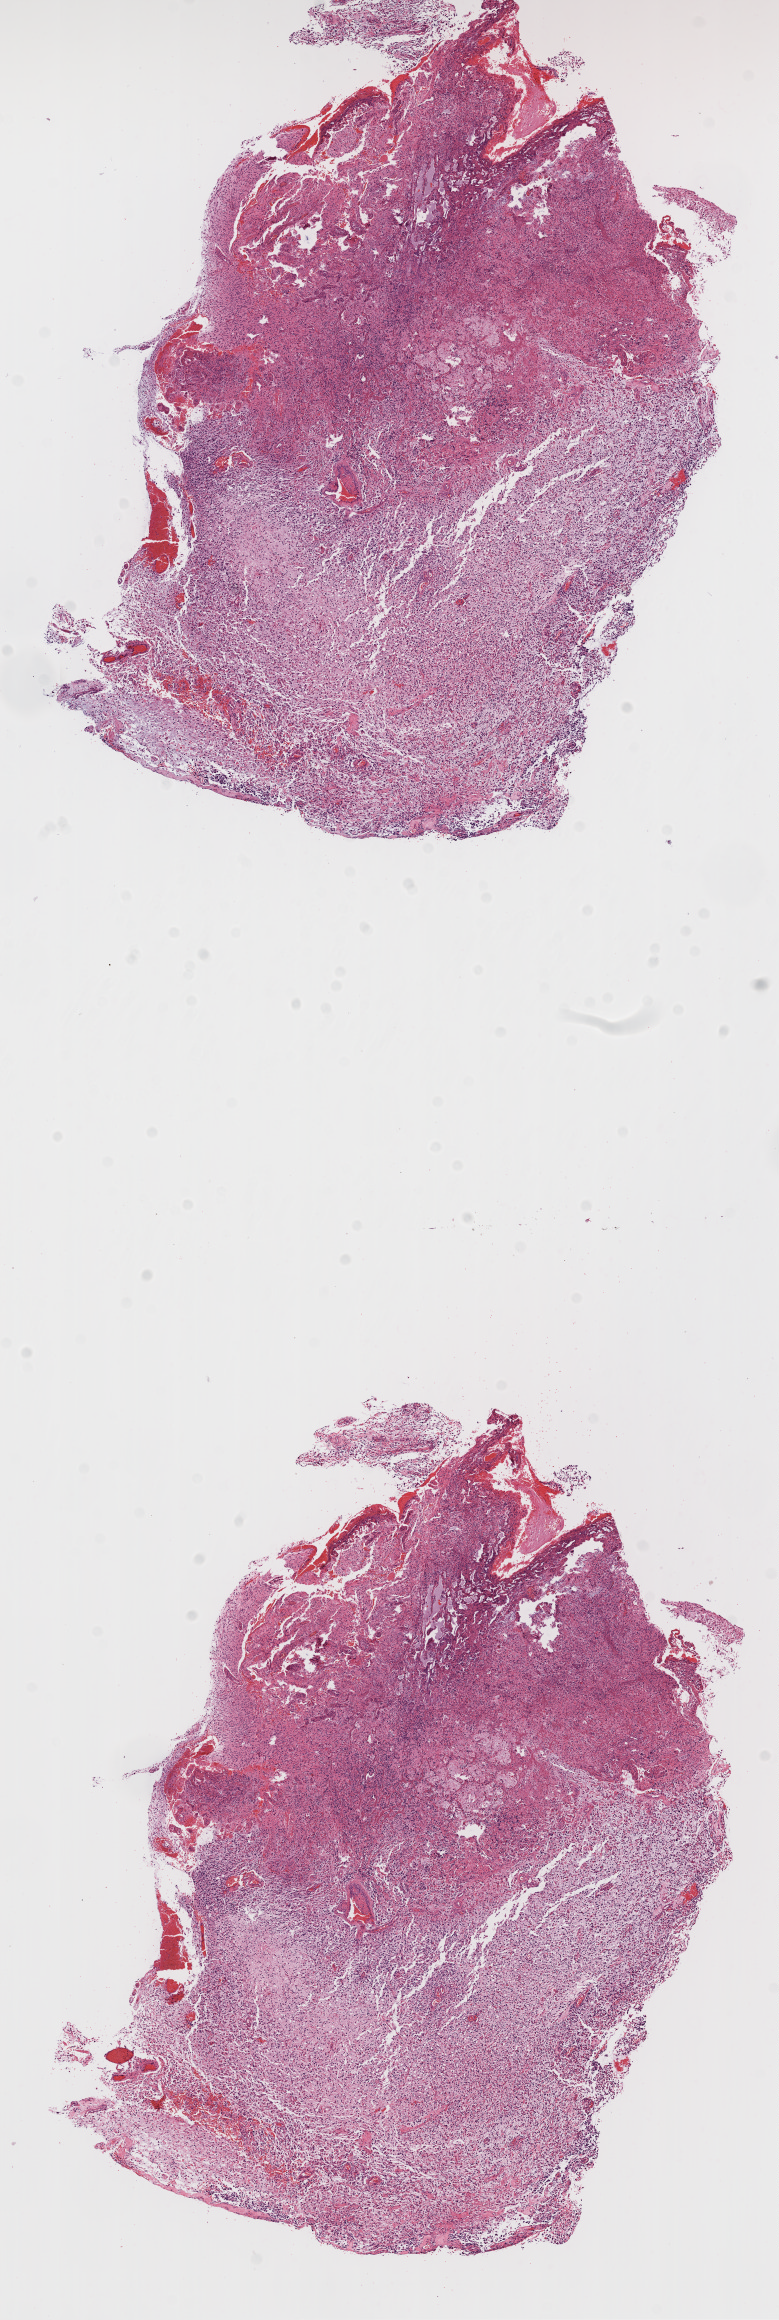
Digitized H&E tissue section (whole slide), a low-resolution overview of the entire scanned area, about 6.3 x 18.7 mm (acquisition: 20x scan), formalin-fixed paraffin-embedded (FFPE) diagnostic section, brain, primary tumour sample. Patient: male, age at initial diagnosis 66 years.
Pathologic diagnosis: Glioblastoma.